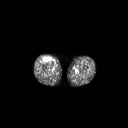
FDG PET of an extremity soft-tissue mass (from a PET/CT study), one axial slice; position 246 of 311 along the scan axis; 3.27 mm slice thickness; 128 × 128 image matrix, field of view 700 × 700 mm. Patient: male, 56 years. From the clinical record (not read from this slice): histological type: pleiomorphic leiomyosarcoma; grade: intermediate; site of the primary tumour: right thigh.
Outlined on this slice (expert contour drawn on MRI and transferred to this co-registered scan by the dataset authors):
- gross tumour volume including surrounding oedema: box from (x=44, y=56) to (x=51, y=62) px